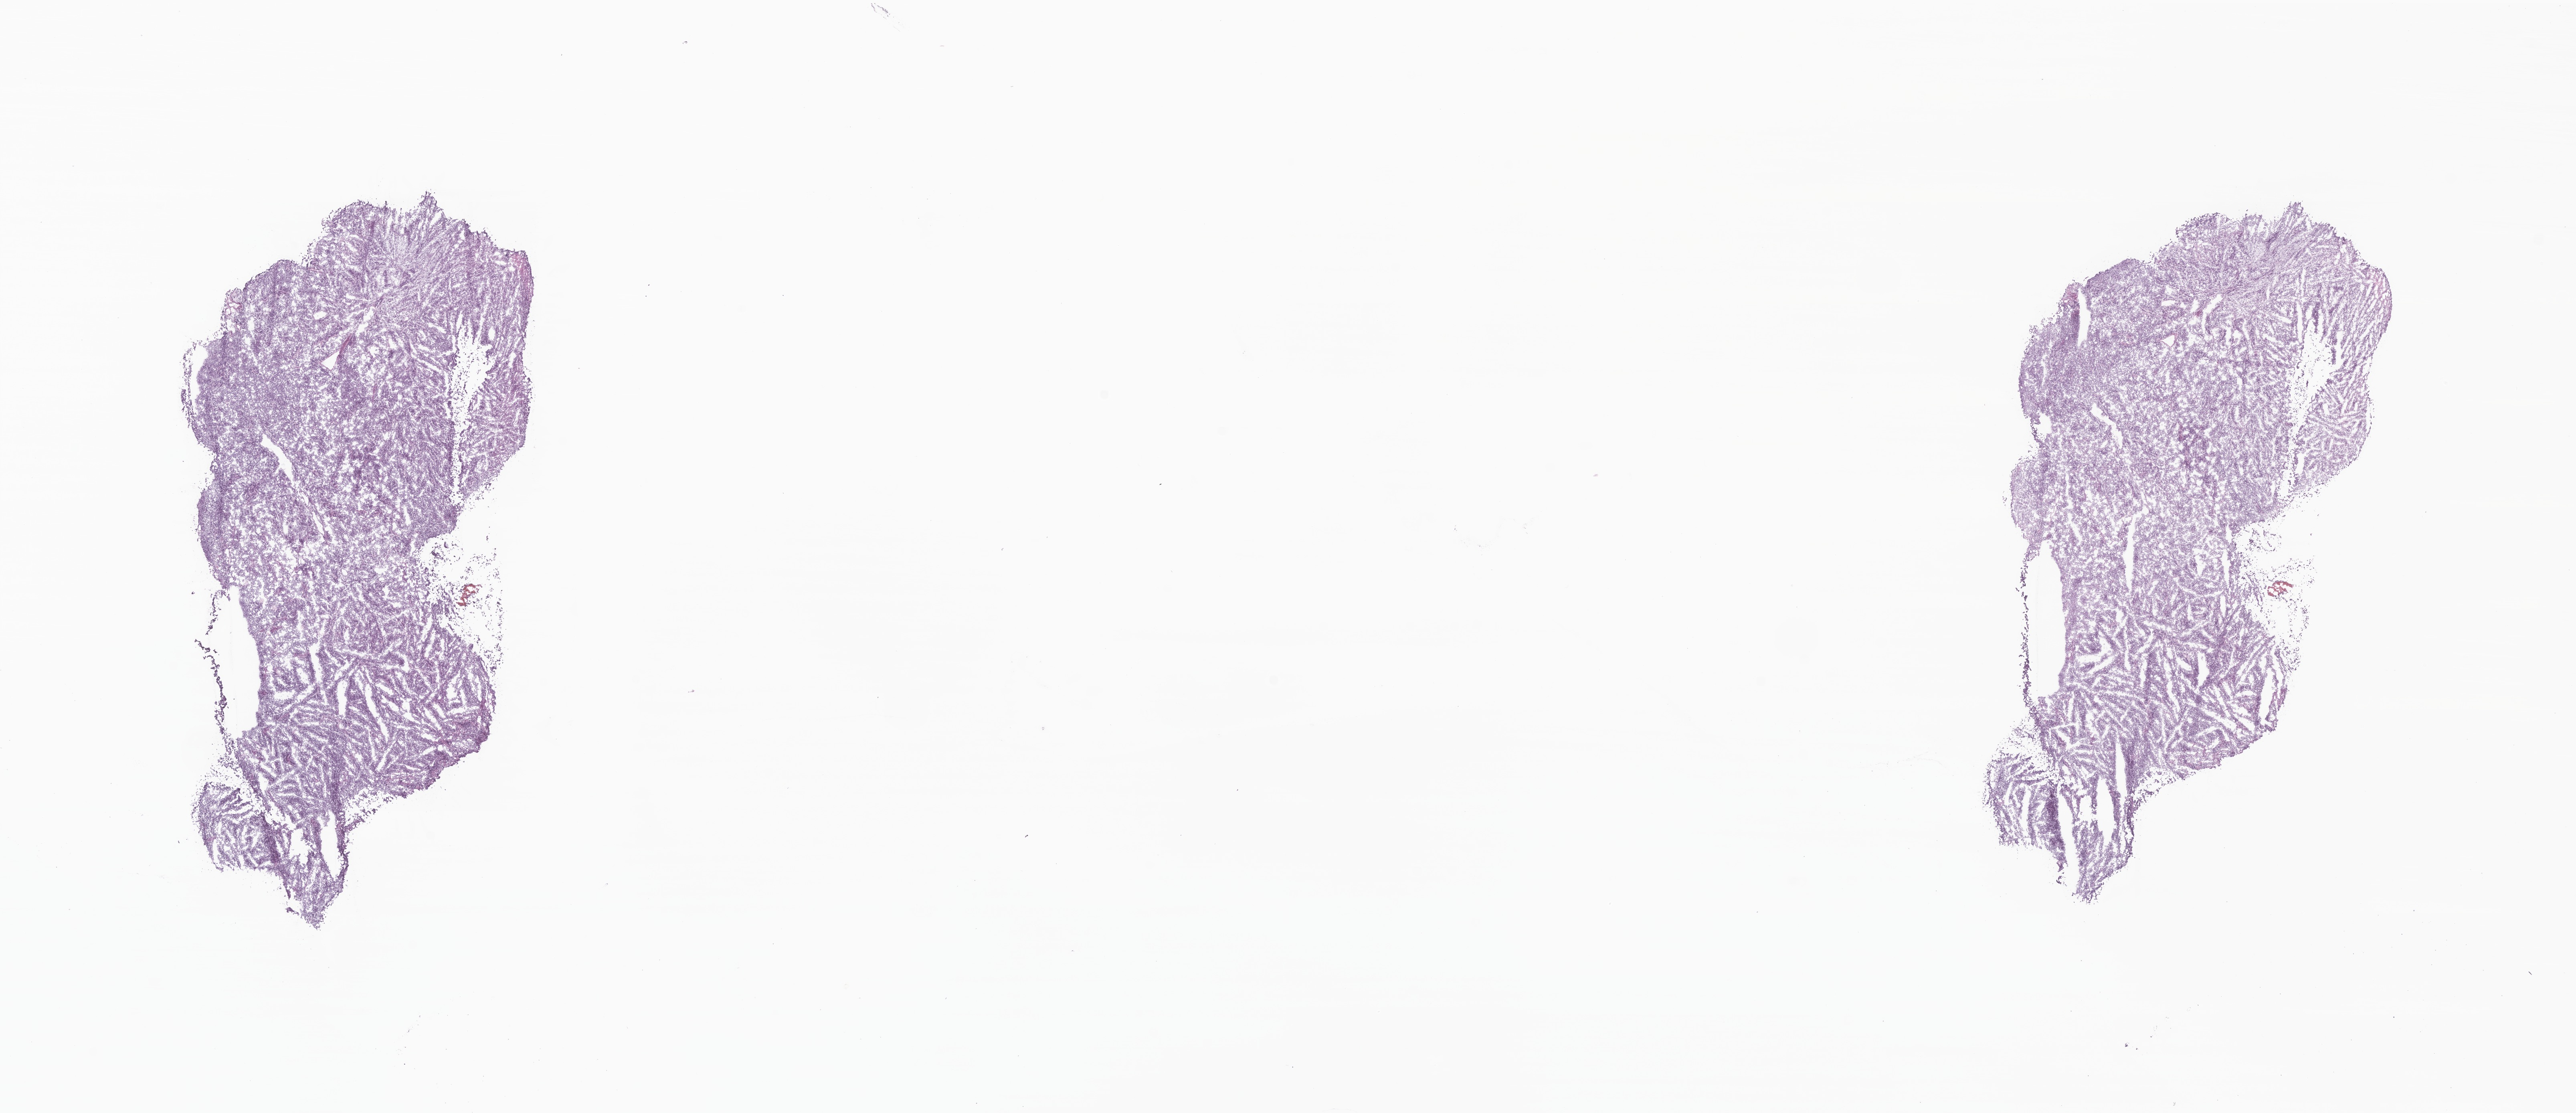
Digitized haematoxylin and eosin-stained section of tumor tissue from the brain, whole scanned area (about 27.1 x 11.7 mm) shown as a low-resolution overview, frozen section (OCT-embedded). Patient: female, age 243 days.
Recorded diagnosis: Atypical teratoid/rhabdoid tumor.